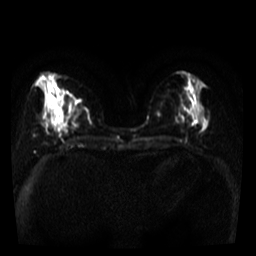
Breast MRI, one axial slice. Slice 17 of 39 in the series (ordered by position). Diffusion-weighted series; image 2 of 4 stored at this slice position (different b-values; order by instance number). 3 T. 5 mm slice thickness. 256 × 256 image matrix, field of view 280 × 280 mm. Female patient.
Annotated regions visible in this slice (outlined manually by an expert reader):
- tumour on diffusion-weighted imaging: box from (x=59, y=99) to (x=66, y=112) px